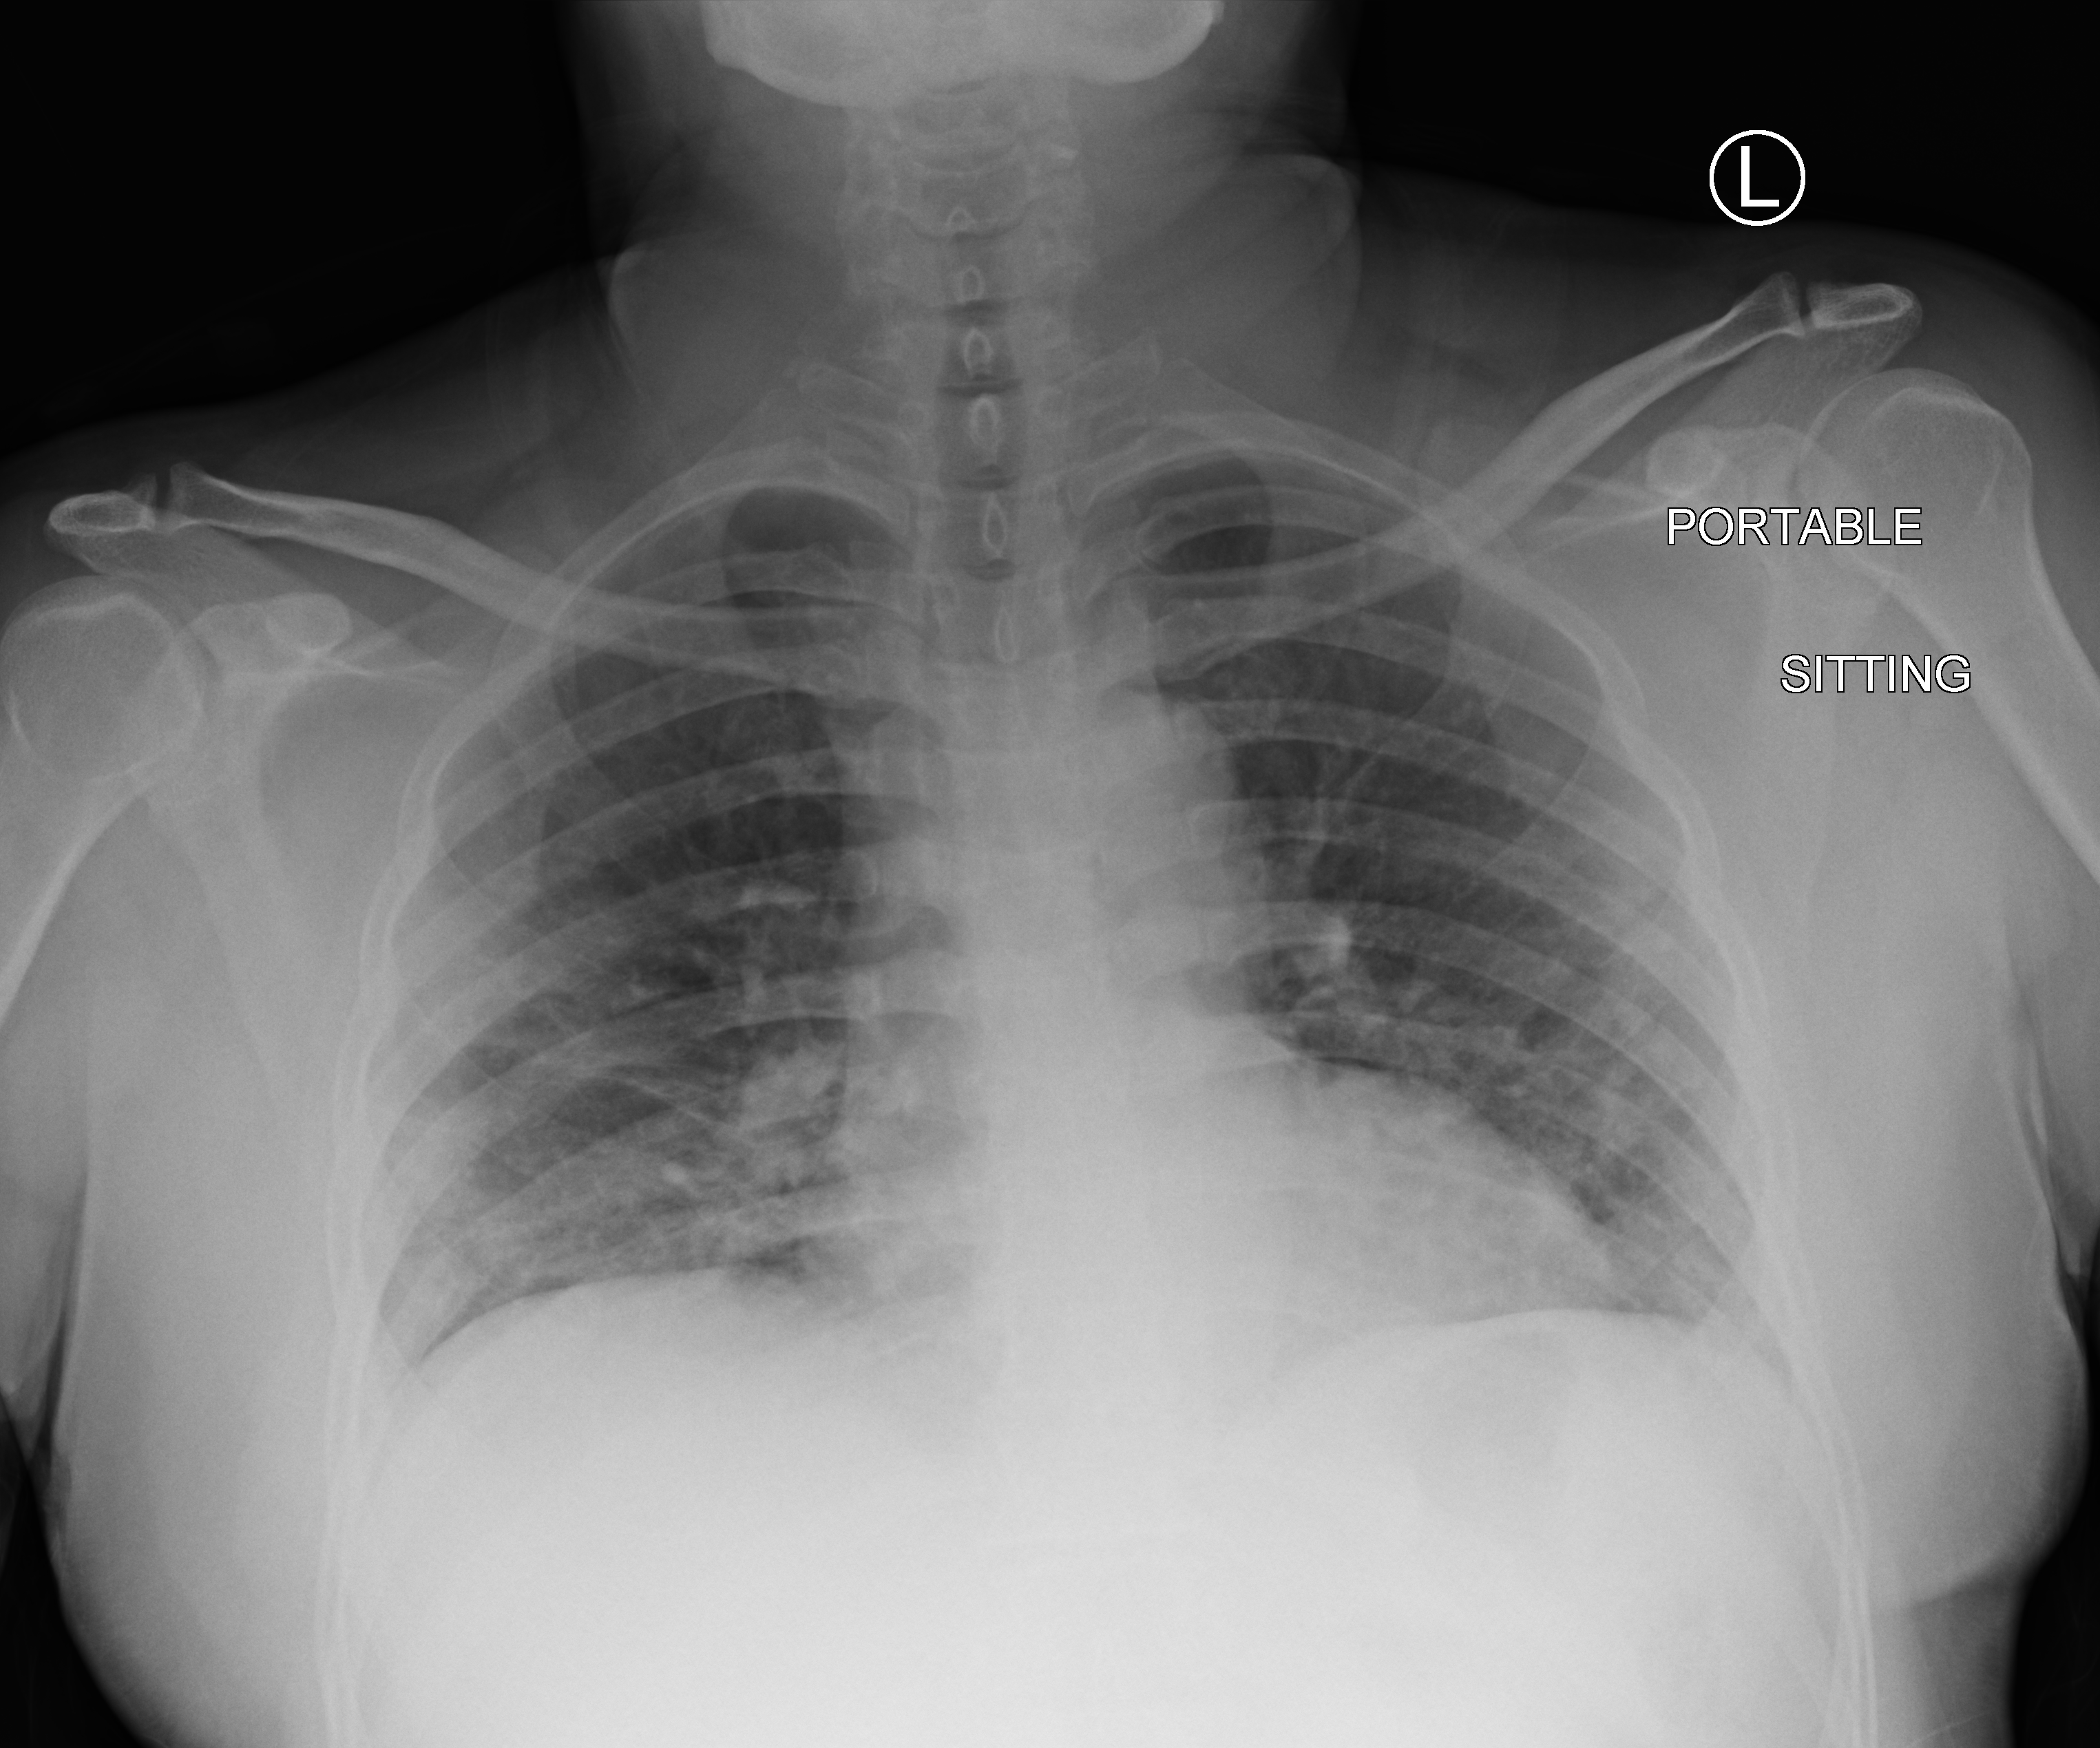
Portable chest radiograph, anteroposterior (AP) projection. Patient hospitalised with COVID-19; male, aged 18–59 years.
Hospital-stay facts (about this admission, not read from this image; timing relative to this image not recorded): admitted to intensive care during this hospital stay: no; other chronic lung disease (admission record): no; mechanically ventilated during this hospital stay: no.